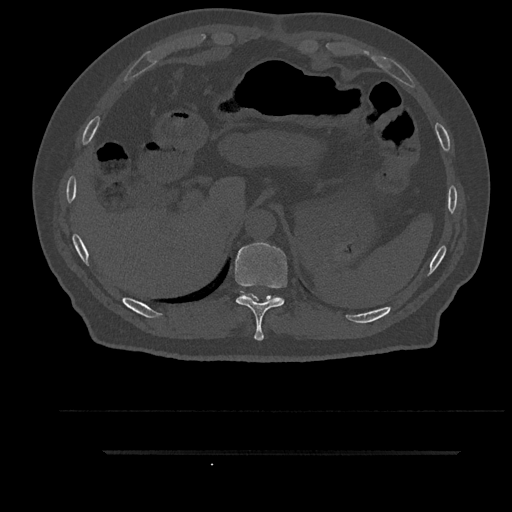
CT including the spine, one axial slice. Reconstruction kernel Br40s/3. Bone window (W 1800 / L 400 HU). 0.5 mm slice thickness. 512 × 512 image matrix. Male patient, age 63 years. Case-level facts recorded for this patient, not image findings: primary cancer: renal.
Annotated regions visible in this slice (semi-automatically segmented with operator editing):
- T10 vertebra: bounding box [x1, y1, x2, y2] px = [235, 242, 288, 341]
- T11 vertebra: [241, 291, 279, 299]